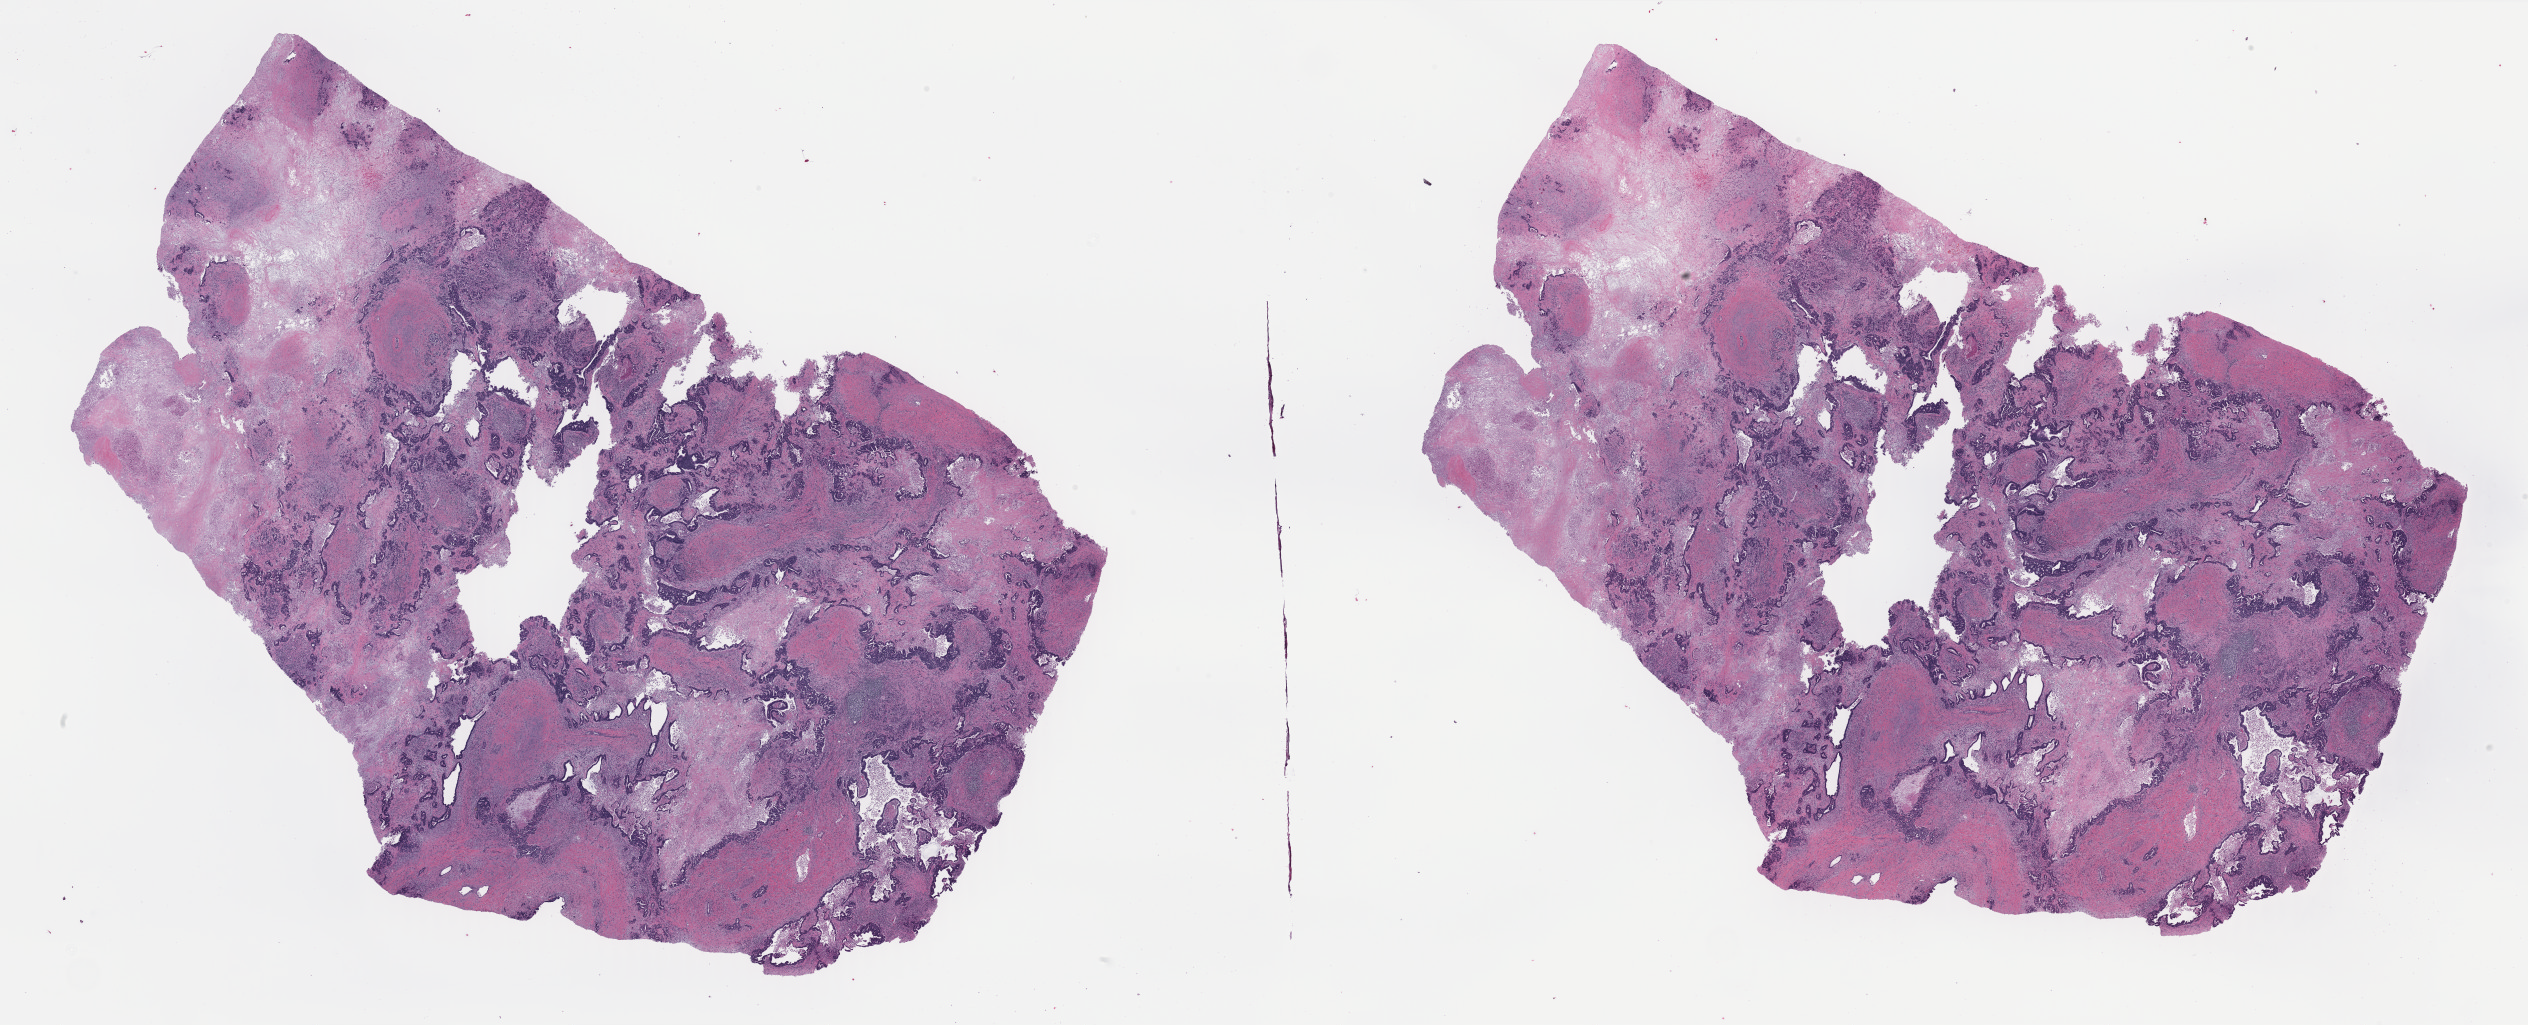
Whole-slide histology image, Hematoxylin and eosin (H&E) stained, whole scanned area (about 40.0 x 16.2 mm, acquisition: 40x scan) shown as a low-resolution overview; formalin-fixed paraffin-embedded (FFPE) diagnostic section; primary tumour sample from the bile duct. Patient: male, age at initial diagnosis 59 years. Histologic grade: G3 (poorly differentiated).
• histologic diagnosis: Cholangiocarcinoma (intrahepatic bile duct)
• TNM: T3 N0 M1
• AJCC pathologic stage: IVB (7th edition)